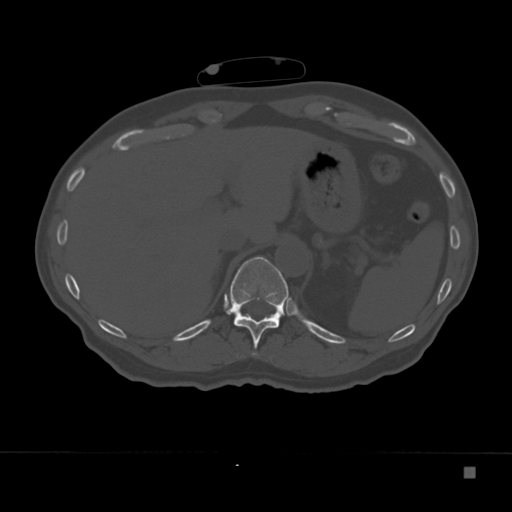
CT including the spine, one axial slice. Slice 151 of 332 in the series (ordered by position). Reconstruction kernel Br40s. 120 kVp. Bone window (W 1800 / L 400 HU). 1.5 mm slice thickness. 512 × 512 image matrix, field of view 389 × 389 mm. Patient: male, 72 years. From the clinical record (not read from this slice): primary cancer: skeletal.
Outlined on this slice (semi-automatically segmented with operator editing):
- T11 vertebra: box from (x=227, y=256) to (x=288, y=356) px
- T12 vertebra: (x=279, y=317)–(x=281, y=321)